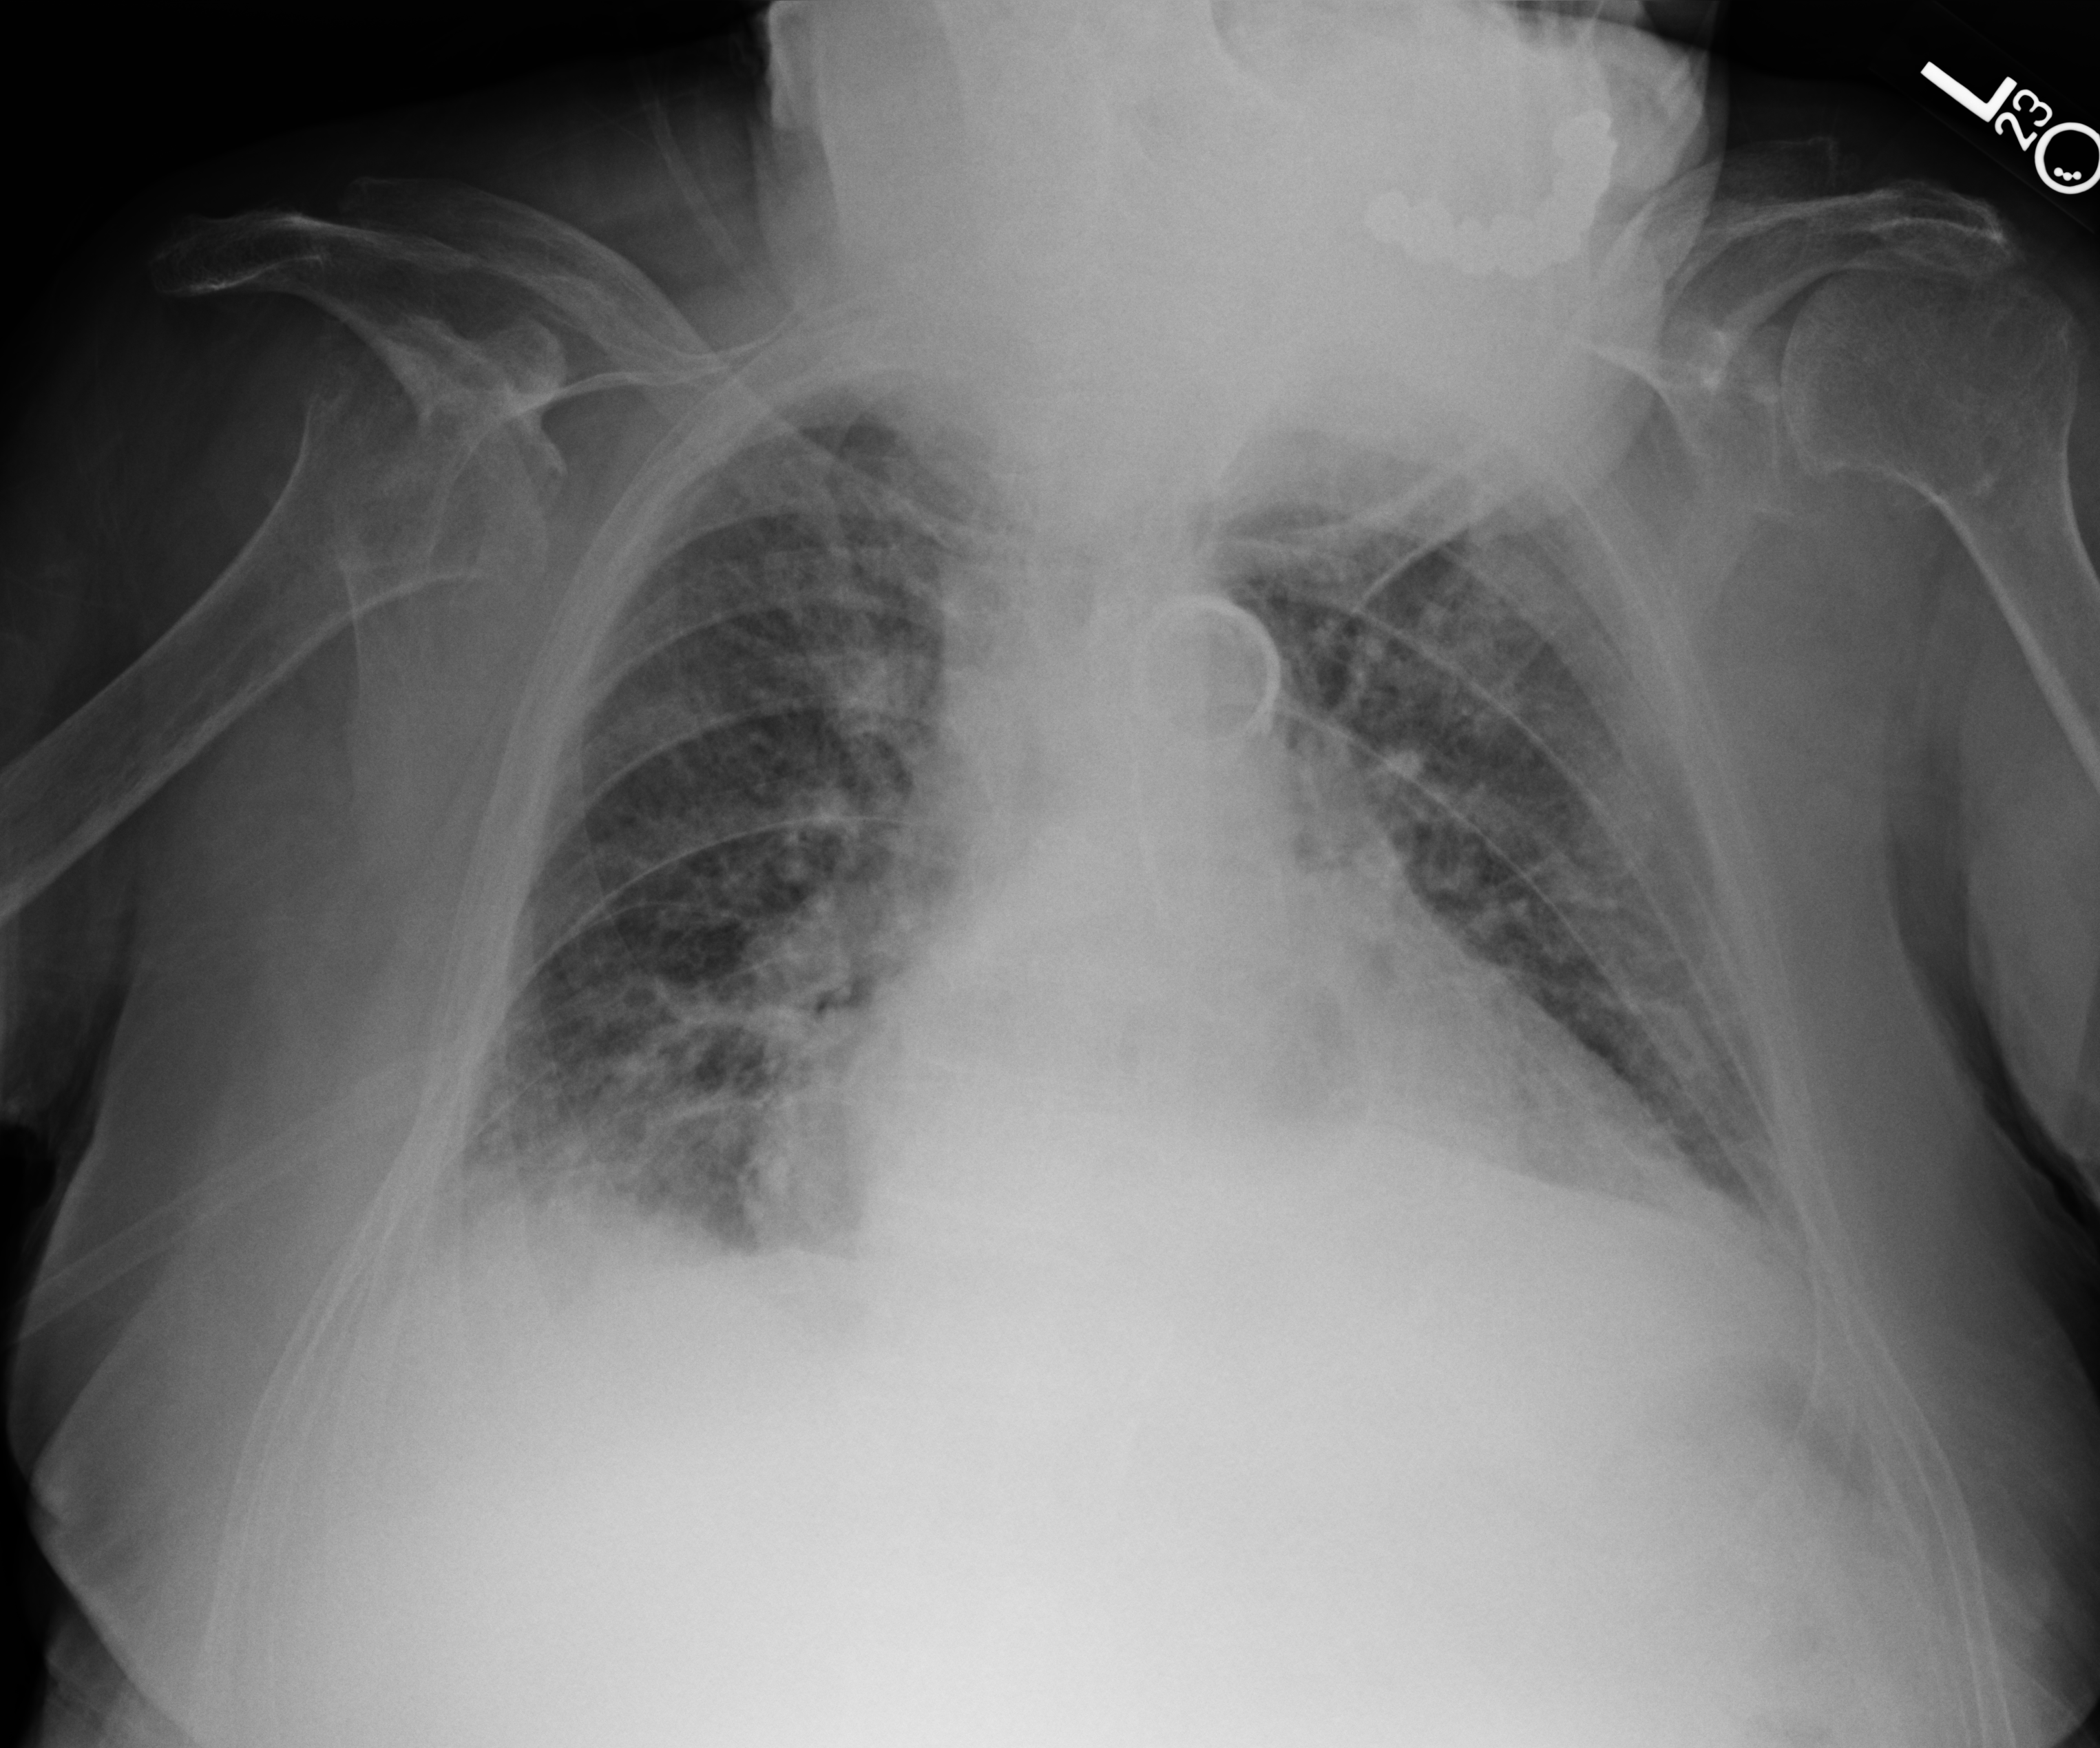
Portable chest radiograph; anteroposterior (AP) projection. Patient hospitalised with COVID-19; male, aged 75–90 years.
Hospital-stay facts (about this admission, not read from this image; timing relative to this image not recorded): mechanically ventilated during this hospital stay: no; length of hospital stay: 10 days; admitted to intensive care during this hospital stay: no.